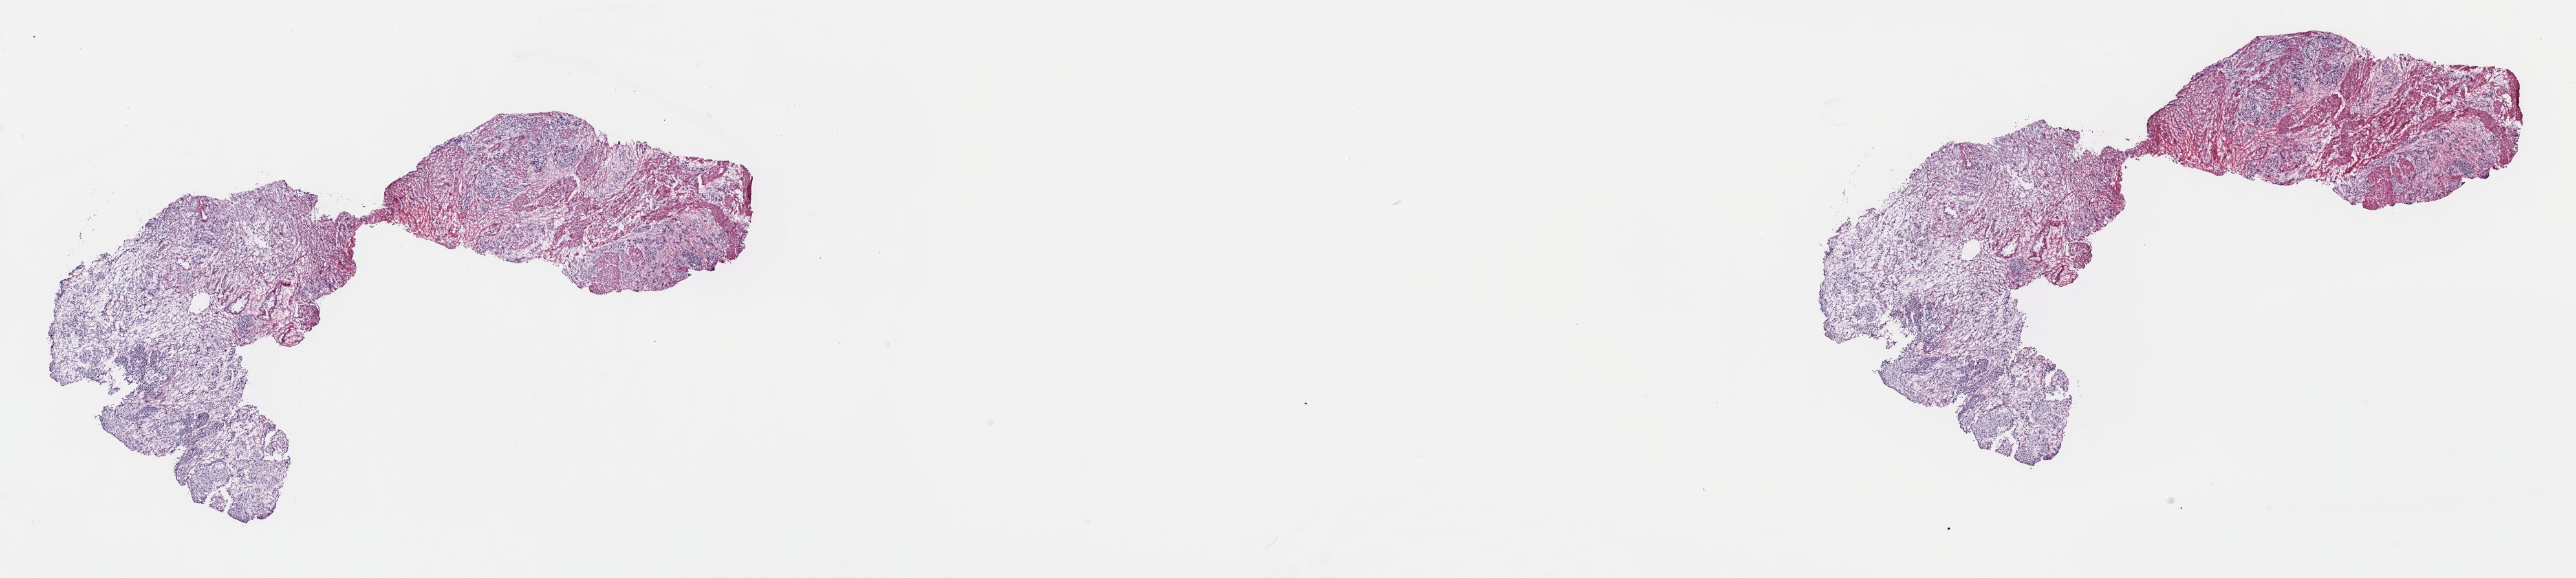
Digitized H&E-stained tissue section (whole slide) — shown as a low-resolution overview of the whole scanned area (about 32.2 x 7.2 mm, slide scanned at 40x), frozen section, sample: primary tumour, bladder. Patient: male, age at initial diagnosis 82 years. Histologic grade: high grade. Pathologist review of this section (percent, as recorded): tumour cells 65%, tumour nuclei 65%, normal cells 10%, stromal cells 25%, necrosis 0%. Infiltration values recorded for this section: lymphocyte infiltration 5%, monocyte infiltration 0%, neutrophil infiltration 0%.
• diagnosis: Transitional cell carcinoma (posterior wall of bladder)
• lymph nodes positive (case pathology): 1 of 7 examined
• AJCC pathologic stage: IV (7th edition)
• TNM: T4 N1 M0